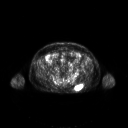
FDG PET of an extremity soft-tissue mass (from a PET/CT study), one axial slice; position 82 of 267 along the scan axis; 3.27 mm slice thickness; 128 × 128 image matrix, field of view 700 × 700 mm. Patient: male, 61 years. Case-level facts recorded for this patient, not image findings: histological type: pleiomorphic leiomyosarcoma; grade: high; site of the primary tumour: left buttock.
Annotated regions visible in this slice (expert contour drawn on MRI and transferred to this co-registered scan by the dataset authors):
- gross tumour volume including surrounding oedema: box from (x=75, y=85) to (x=82, y=90) px
- gross tumour volume (mass): (x=76, y=86)–(x=82, y=90)